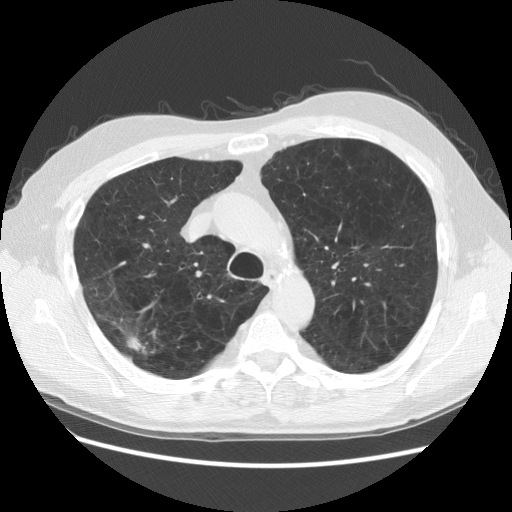
Low-dose screening chest CT, one axial slice. Slice 98 of 137 in the series (ordered by position). Reconstruction kernel STANDARD. 140 kVp. Lung window (W 1500 / L -600 HU). 2.5 mm slice thickness. 512 × 512 image matrix, field of view 377 × 377 mm.
Outlined on this slice (manually delineated by an expert):
- lesion 2 (nodule, upper lobe of right lung): bounding box <126,333,144,351> (left, top, right, bottom; pixels)